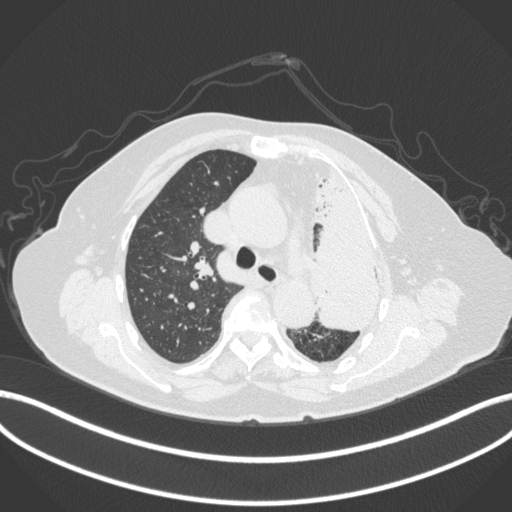
Chest CT, one axial slice; slice 277 of 399 in the series (ordered by position); reconstruction kernel B31f; 120 kVp; lung window (W 1500 / L -600 HU); 1 mm slice thickness; 512 × 512 image matrix, field of view 400 × 400 mm. Patient: female, 75 years. From the clinical record (not read from this slice): clinical TNM (as recorded): T3 N3 M1.
Outlined on this slice (rectangle marked by the reading radiologist):
- lung tumour (recorded histology: adenocarcinoma): bounding box [x1, y1, x2, y2] px = [303, 156, 397, 335]